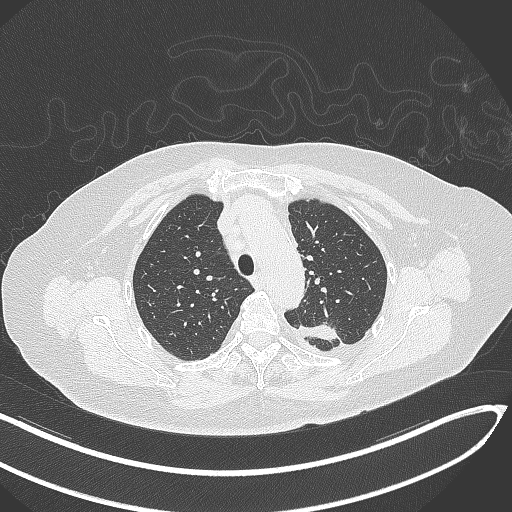
Chest CT, one axial slice. Position 242 of 270 along the scan axis. Lung window (W 1500 / L -600 HU). 1 mm slice thickness. 512 × 512 image matrix, field of view 400 × 400 mm. Patient: female, 76 years. From the clinical record (not read from this slice): clinical TNM (as recorded): T1c N0 M0.
Annotated regions visible in this slice (rectangle marked by the reading radiologist):
- lung tumour (recorded histology: adenocarcinoma): bounding box <292,321,340,347> (left, top, right, bottom; pixels)